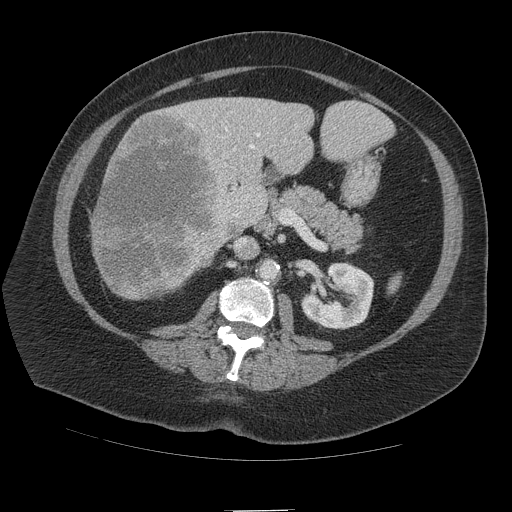
Contrast-enhanced abdominal CT (liver protocol), one axial slice. Position 46 of 109 along the scan axis. Reconstruction kernel STANDARD. 140 kVp. Soft-tissue window (W 400 / L 40 HU). 2.5 mm slice thickness. 512 × 512 image matrix. From the clinical record (not read from this slice): diagnosis: hepatocellular carcinoma (patient treated with transarterial chemoembolisation; whether this scan precedes or follows treatment is not stated here); TNM stage (as recorded): Stage-IVB; Child-Pugh class: A; tumour nodularity: multinodular.
Structures marked on this image (semi-automatic segmentation, software-assisted and operator-edited):
- liver parenchyma outside the tumour (the mass and vessels are separate outlines, so this box may not span the whole liver): bounding box <92,96,368,296> (left, top, right, bottom; pixels)
- mass: <90,106,232,299>
- liver vessels: <224,110,261,217>